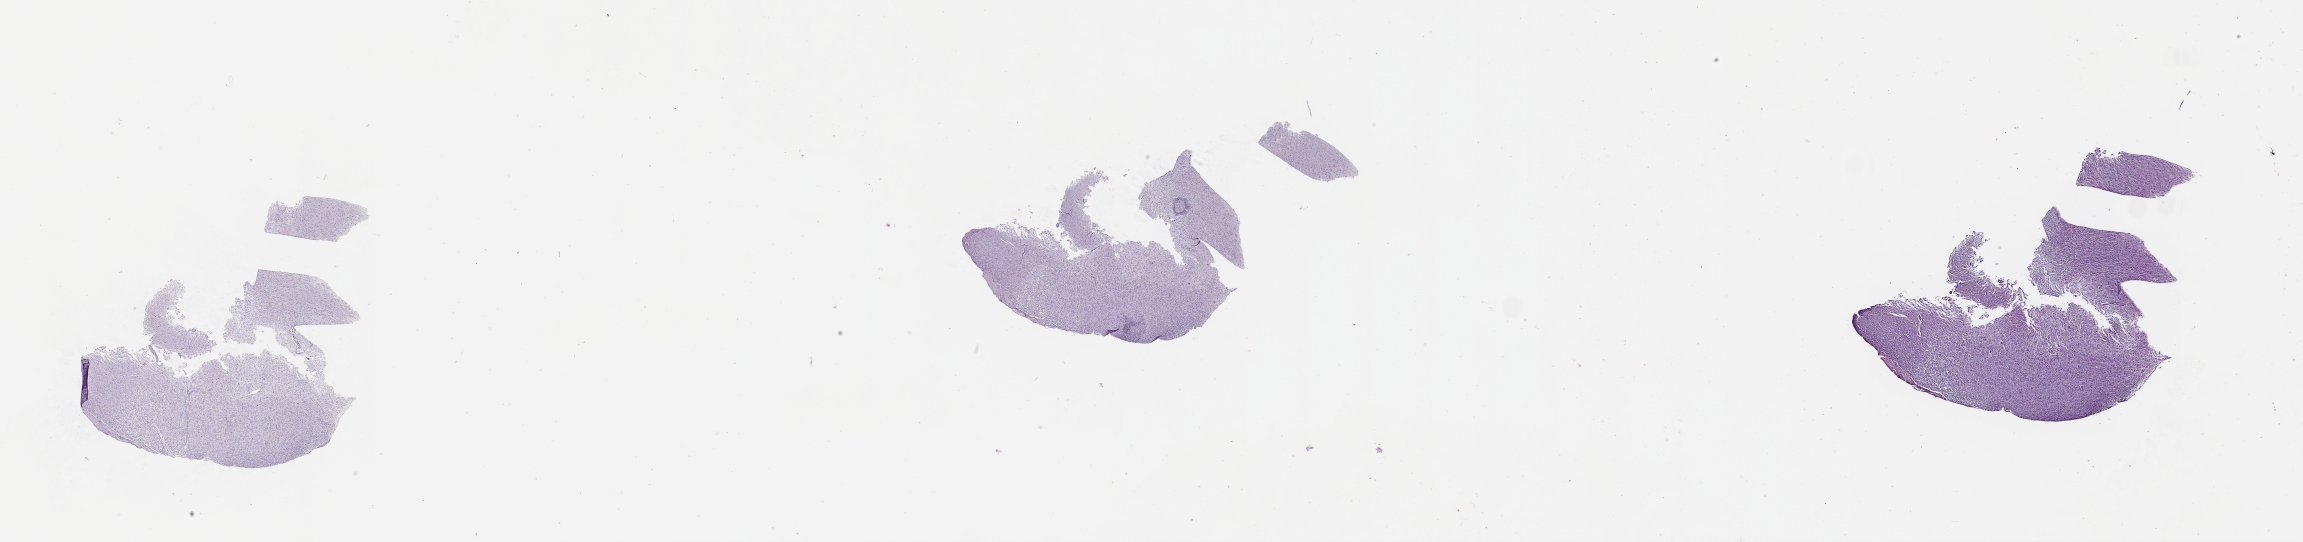
Digitized H&E-stained tissue section (whole slide), whole scanned area (about 37.1 x 8.7 mm, slide scanned at 20x) shown as a low-resolution overview. Tumour tissue sample, sampled site: brain. Female, 81 y/o.
Diagnosis: Glioblastoma.